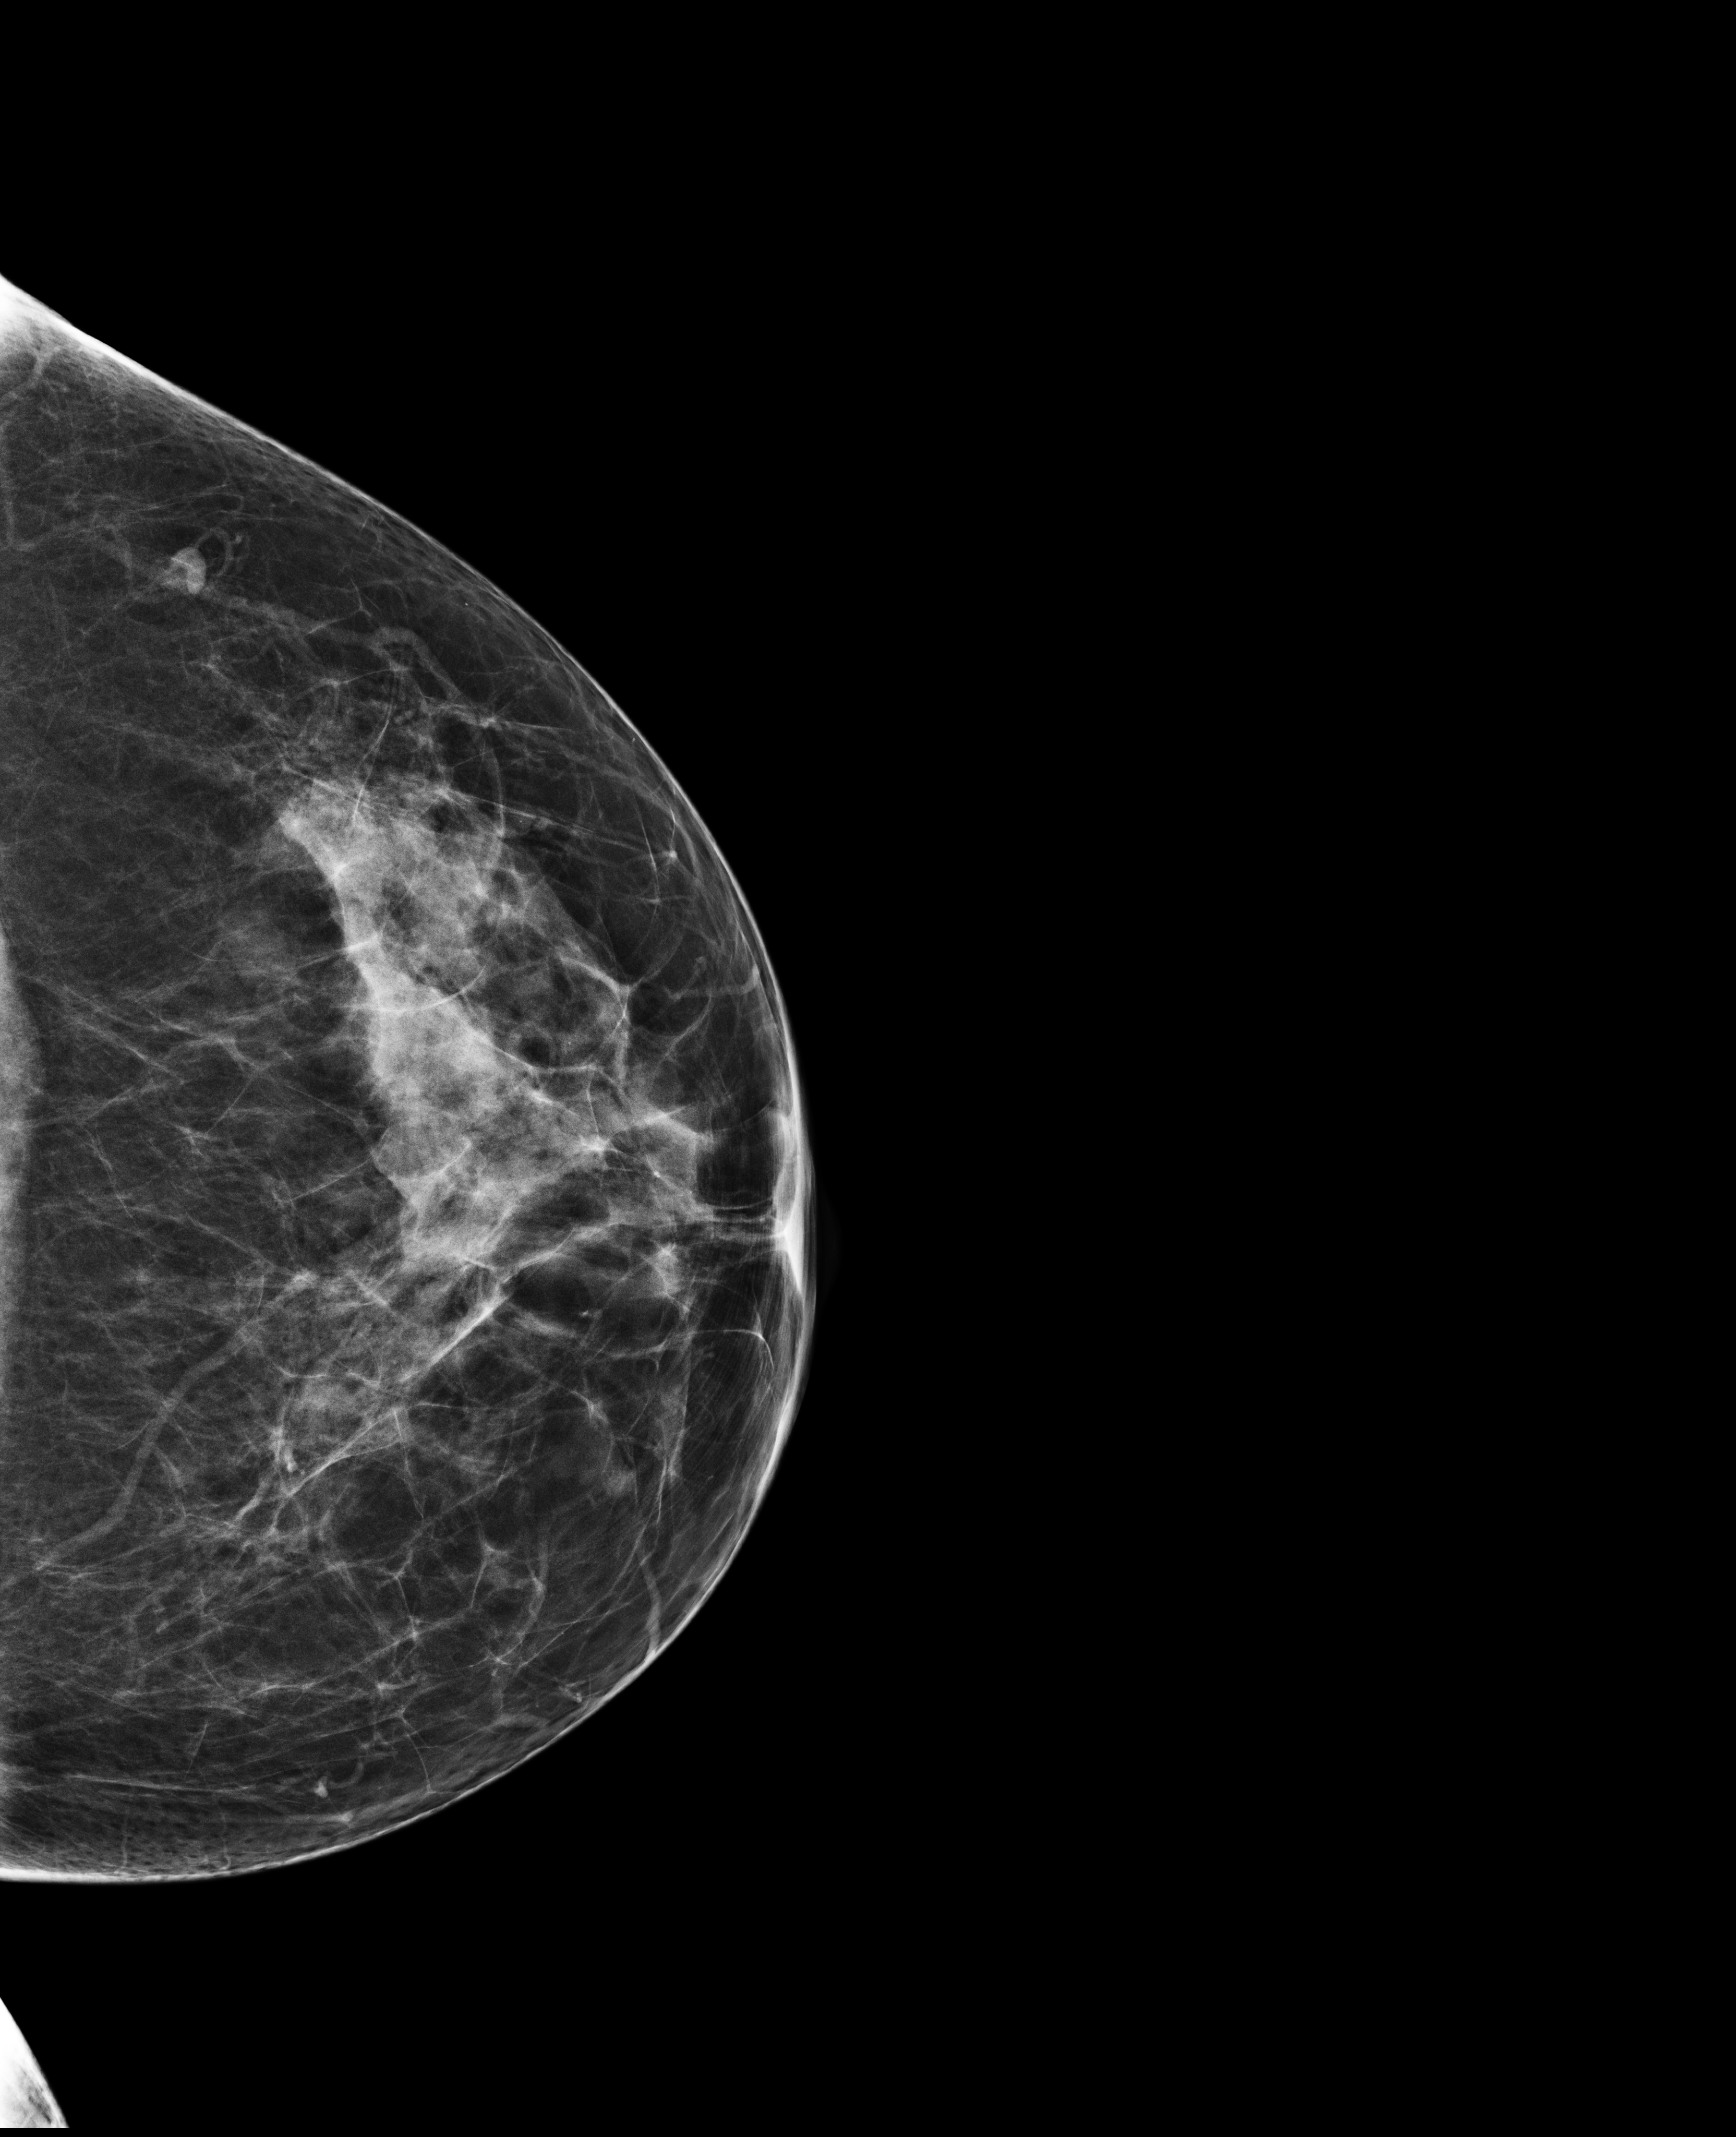
Screening examination, compressed breast thickness 65 mm, system: Selenia Dimensions. Female patient, age 44 years.
Image type: full-field digital mammogram. Breast: left. Projection: CC view.